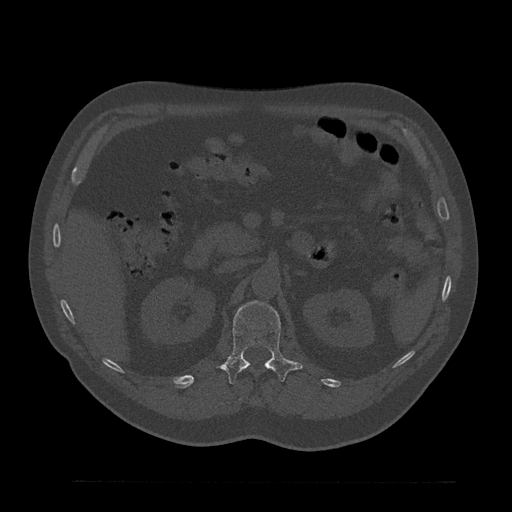
CT including the spine, one axial slice. Position 176 of 797 along the scan axis. Reconstruction kernel Br40s/3. 120 kVp. Bone window (W 1800 / L 400 HU). 0.5 mm slice thickness. 512 × 512 image matrix. Male patient, age 61 years. From the clinical record (not read from this slice): primary cancer: prostate.
Annotated regions visible in this slice (semi-automatic segmentation, software-assisted and operator-edited):
- L1 vertebra: box from (x=222, y=301) to (x=303, y=385) px